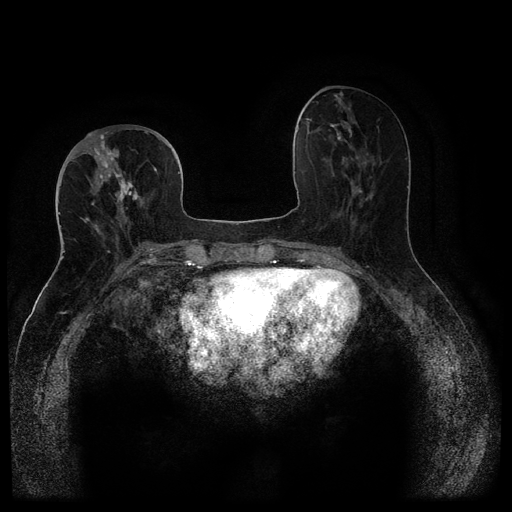
Breast MRI (dynamic contrast-enhanced, multi-phase), one axial slice. Position 44 of 116 along the scan axis. Dynamic contrast-enhanced series, time point 2 of 5 at this slice position (early post-contrast). 1.5 T. TE 2.6 ms, TR 5.4 ms. 512 × 512 image matrix. Female patient, age 68 years.
Structures marked on this image (semi-automatically segmented with operator editing):
- breast lesion (labelled 'tumour' in the annotation; benign lesions carry a separate 'benign' label): box from (x=113, y=168) to (x=141, y=209) px